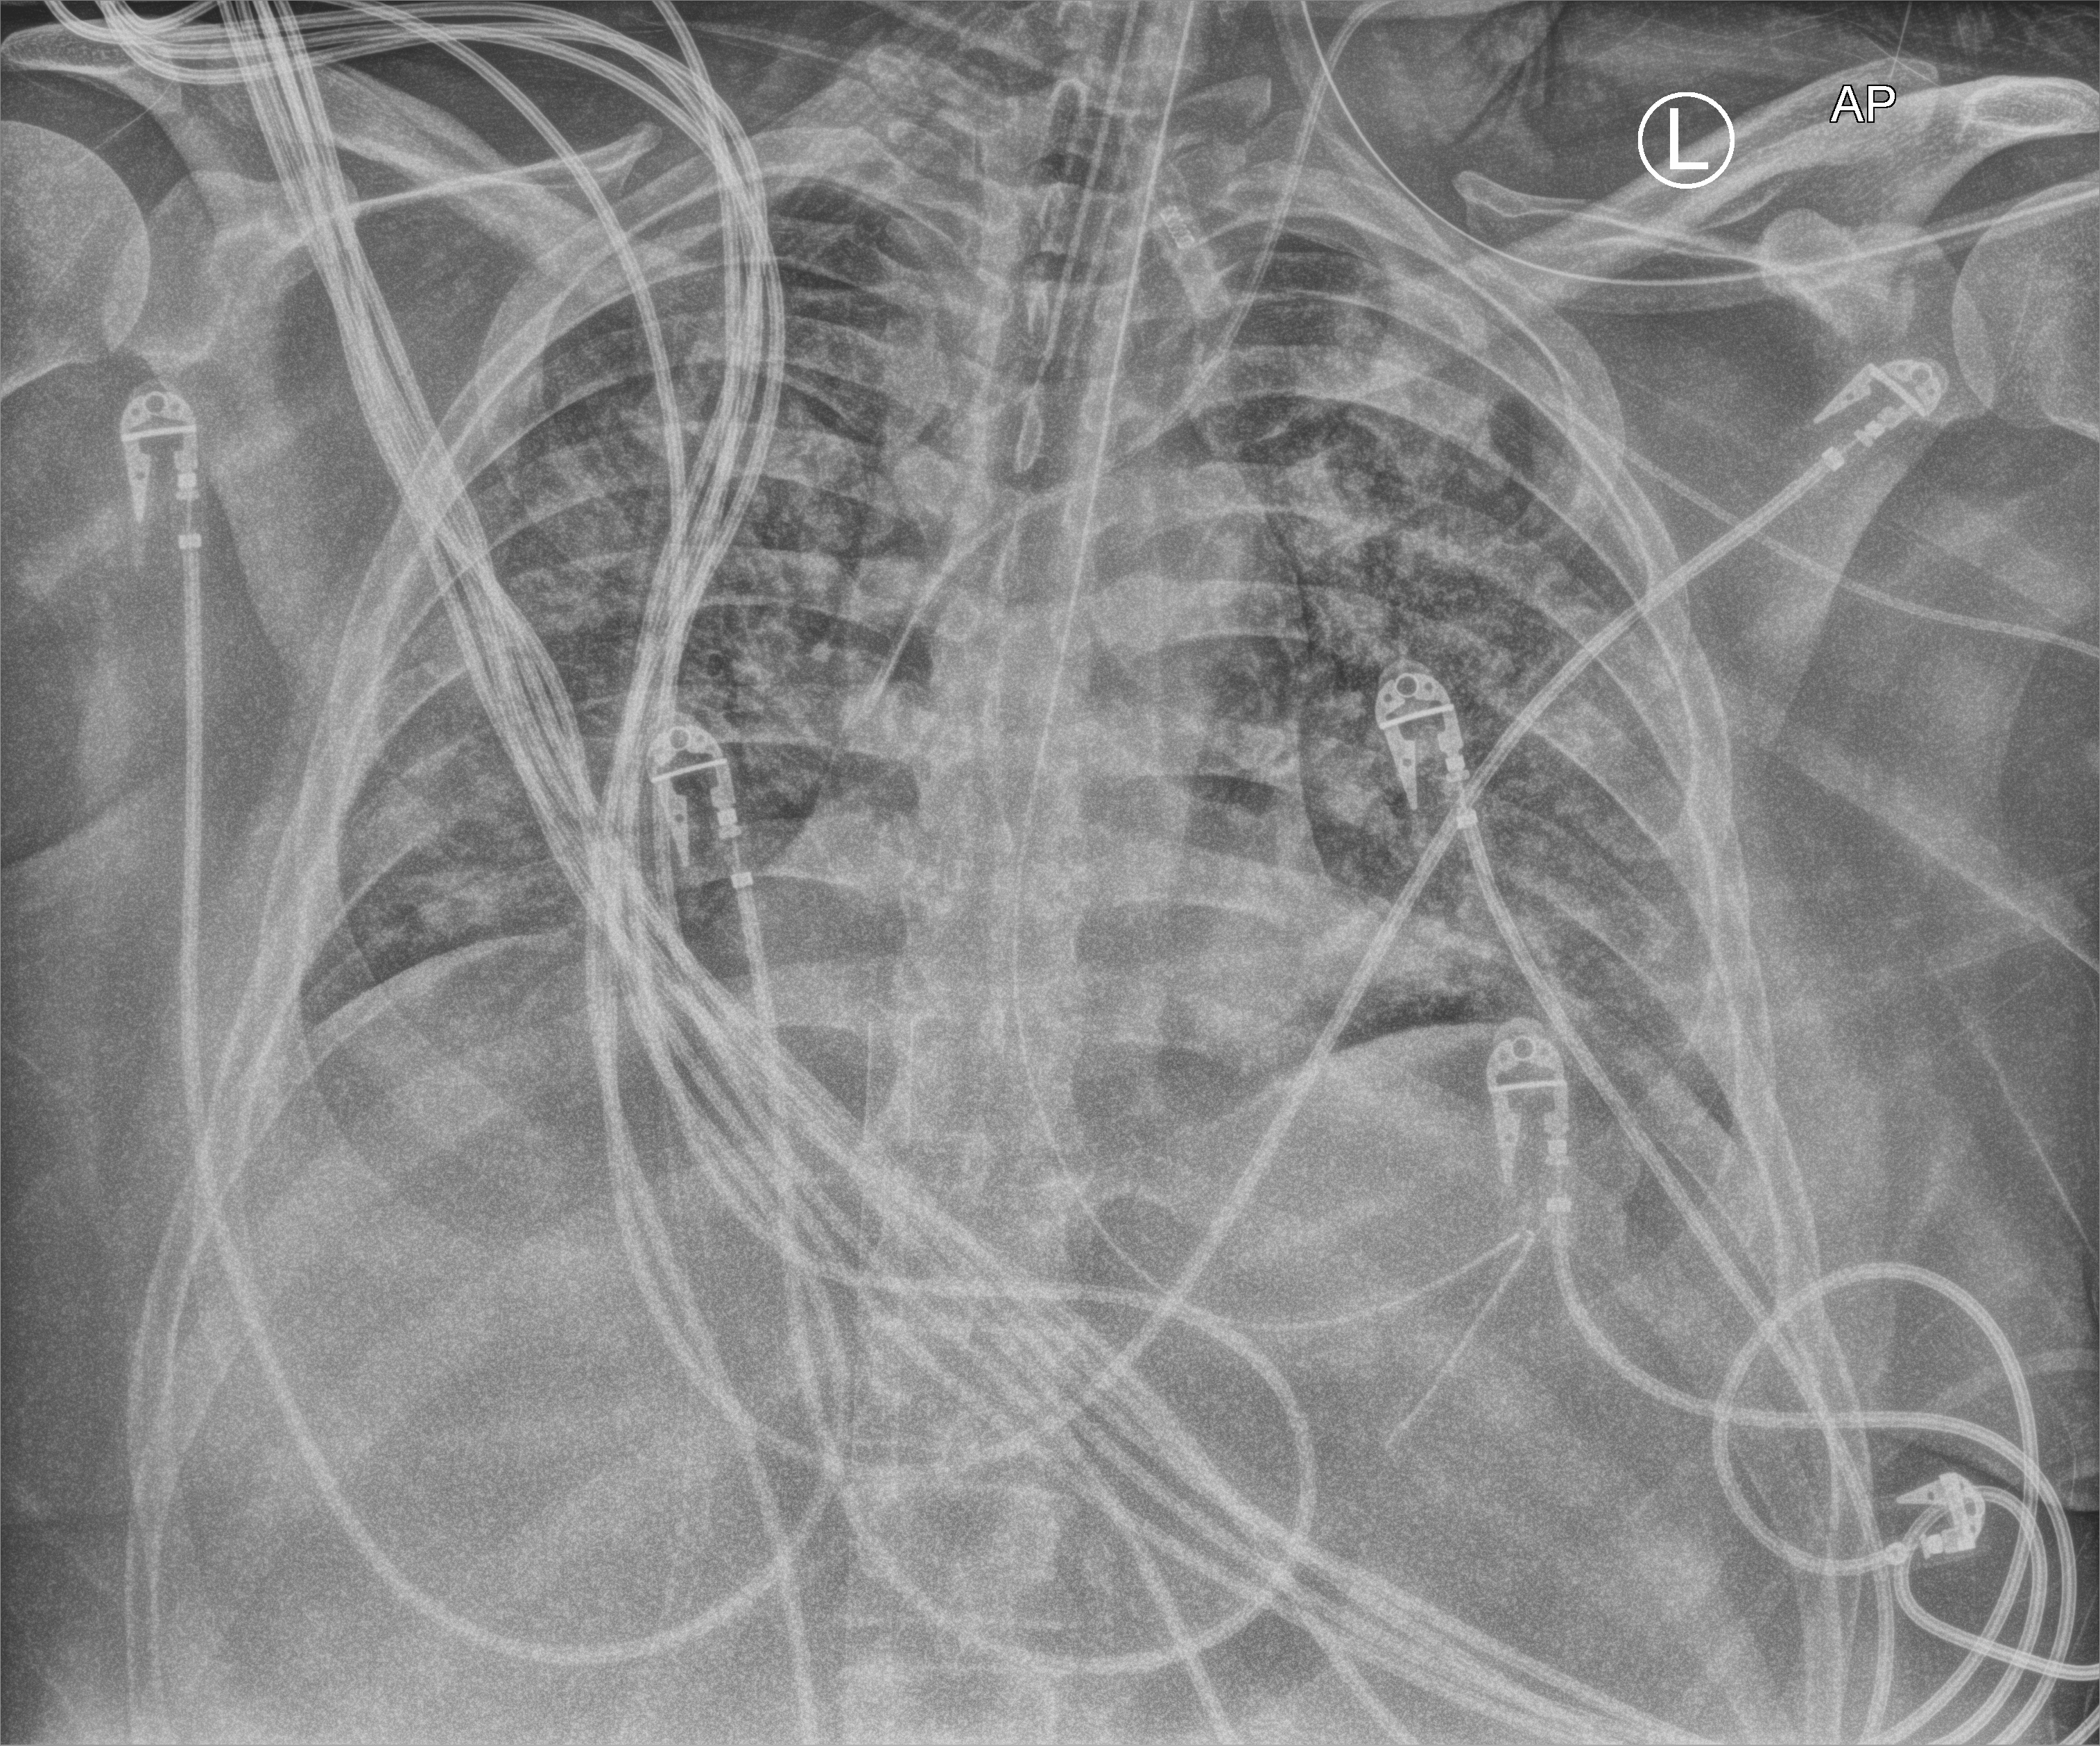
Portable chest radiograph; anteroposterior (AP) projection. Patient hospitalised with COVID-19, aged 18–59 years.
Admission-level facts for this patient (not findings on this image; timing relative to this image not recorded):
- chronic kidney disease (admission record): no
- mechanically ventilated during this hospital stay: yes
- length of hospital stay: 15 days